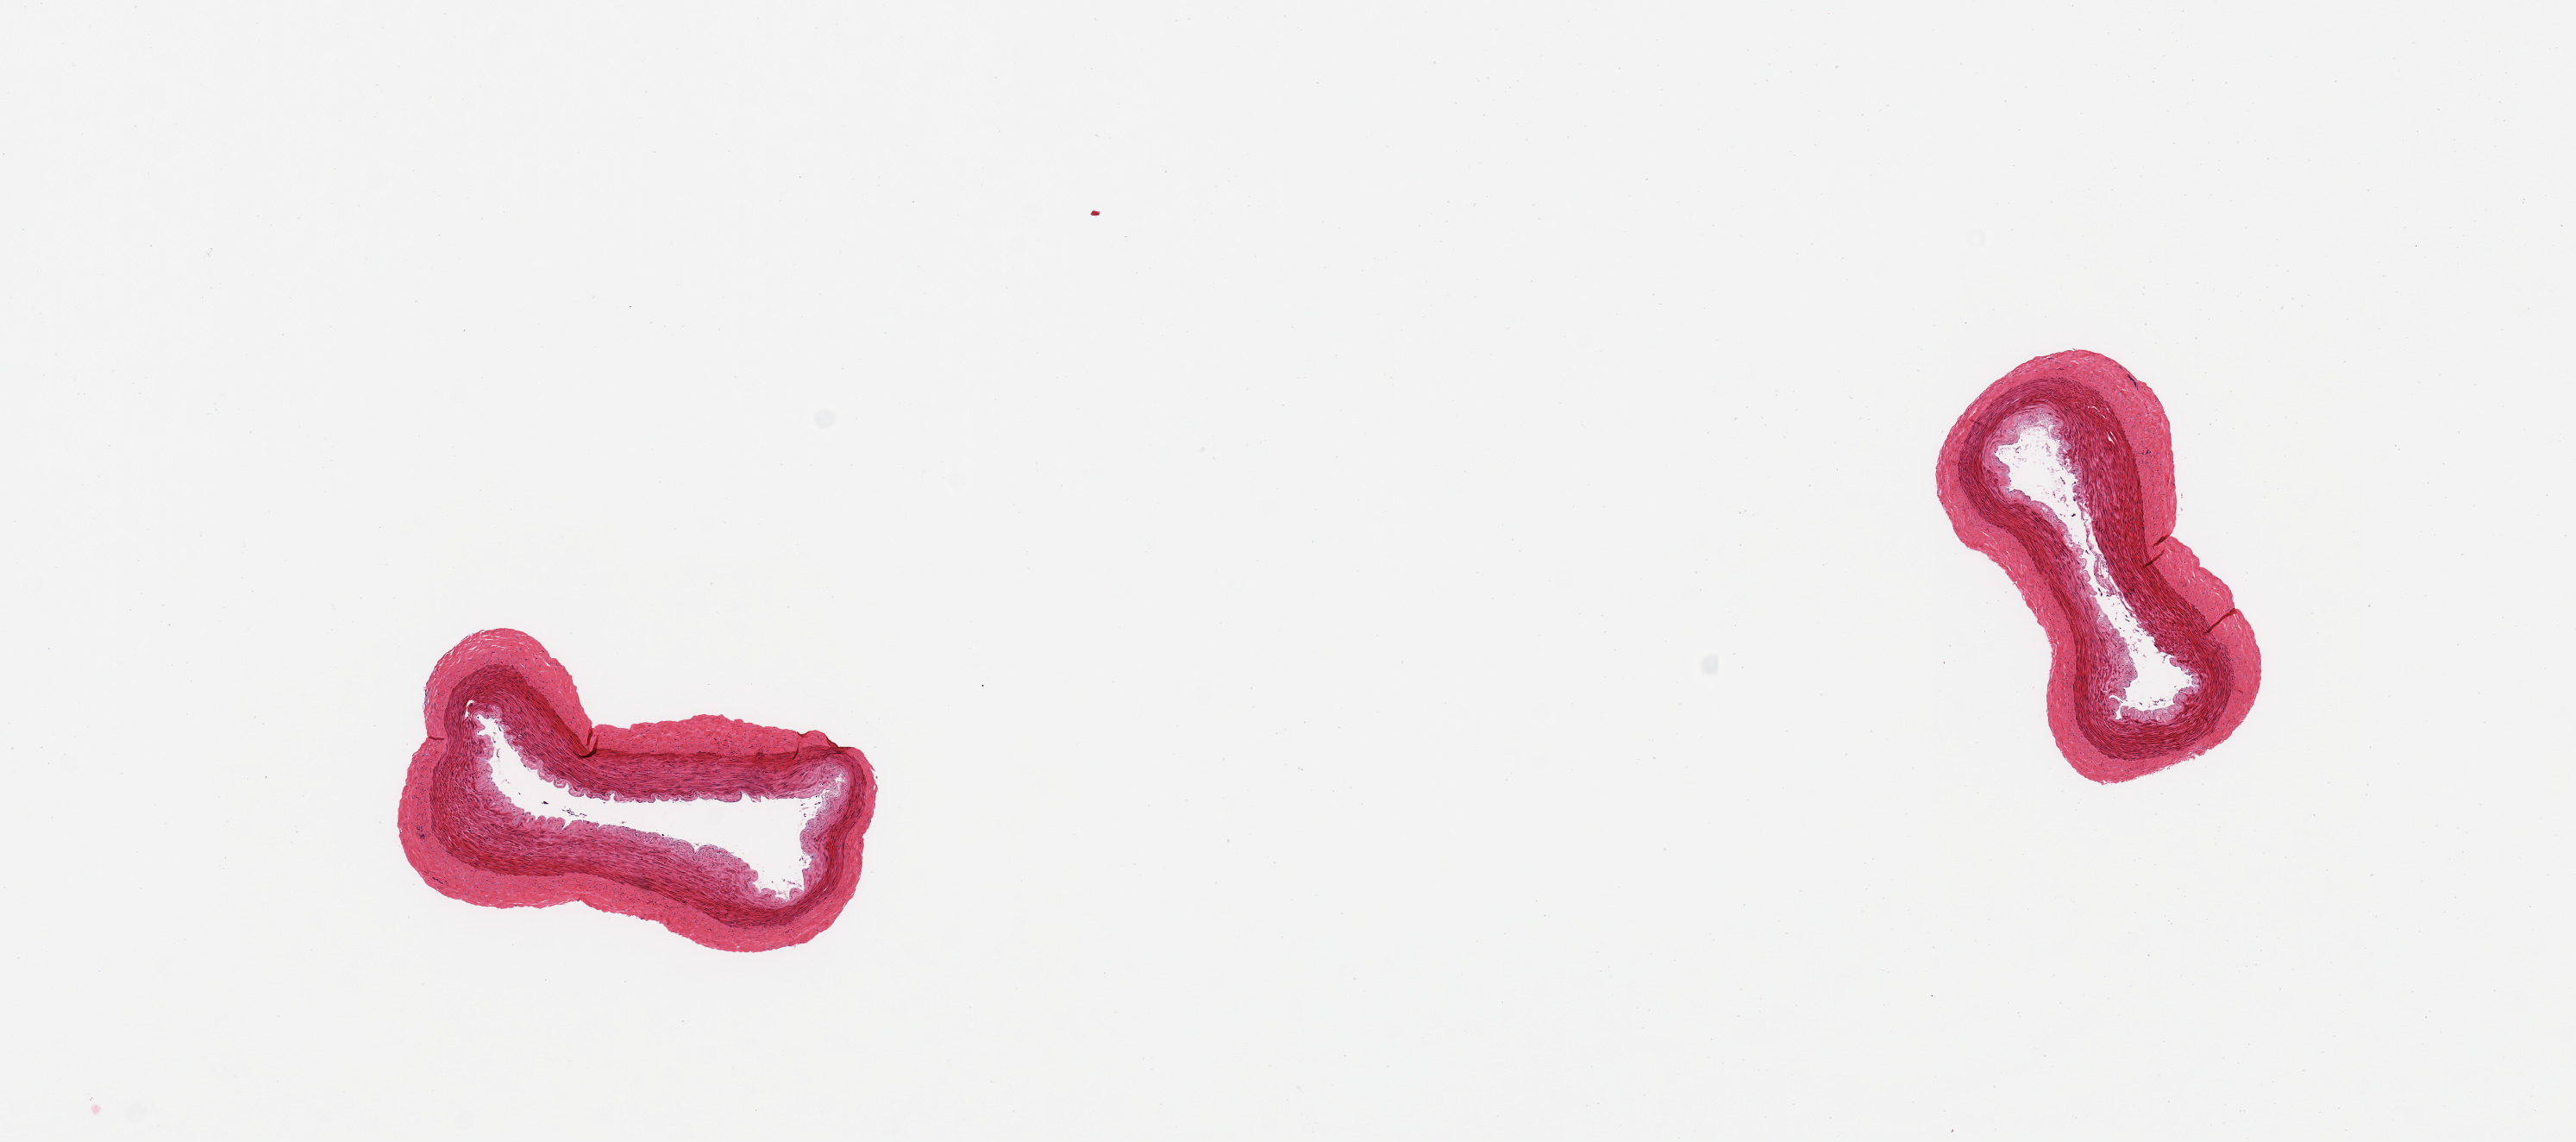
Hematoxylin and eosin (H&E) whole-slide image, brightfield, a low-resolution overview of the entire scanned area, about 11.8 x 5.2 mm. PAXgene-fixed, paraffin-embedded tissue. Section of tibial artery (target tissue). Donor tissue sample. Donor: female.
• pathologist's review note for this sample: 2 pieces; patent; ~0.2mm attached adventitia